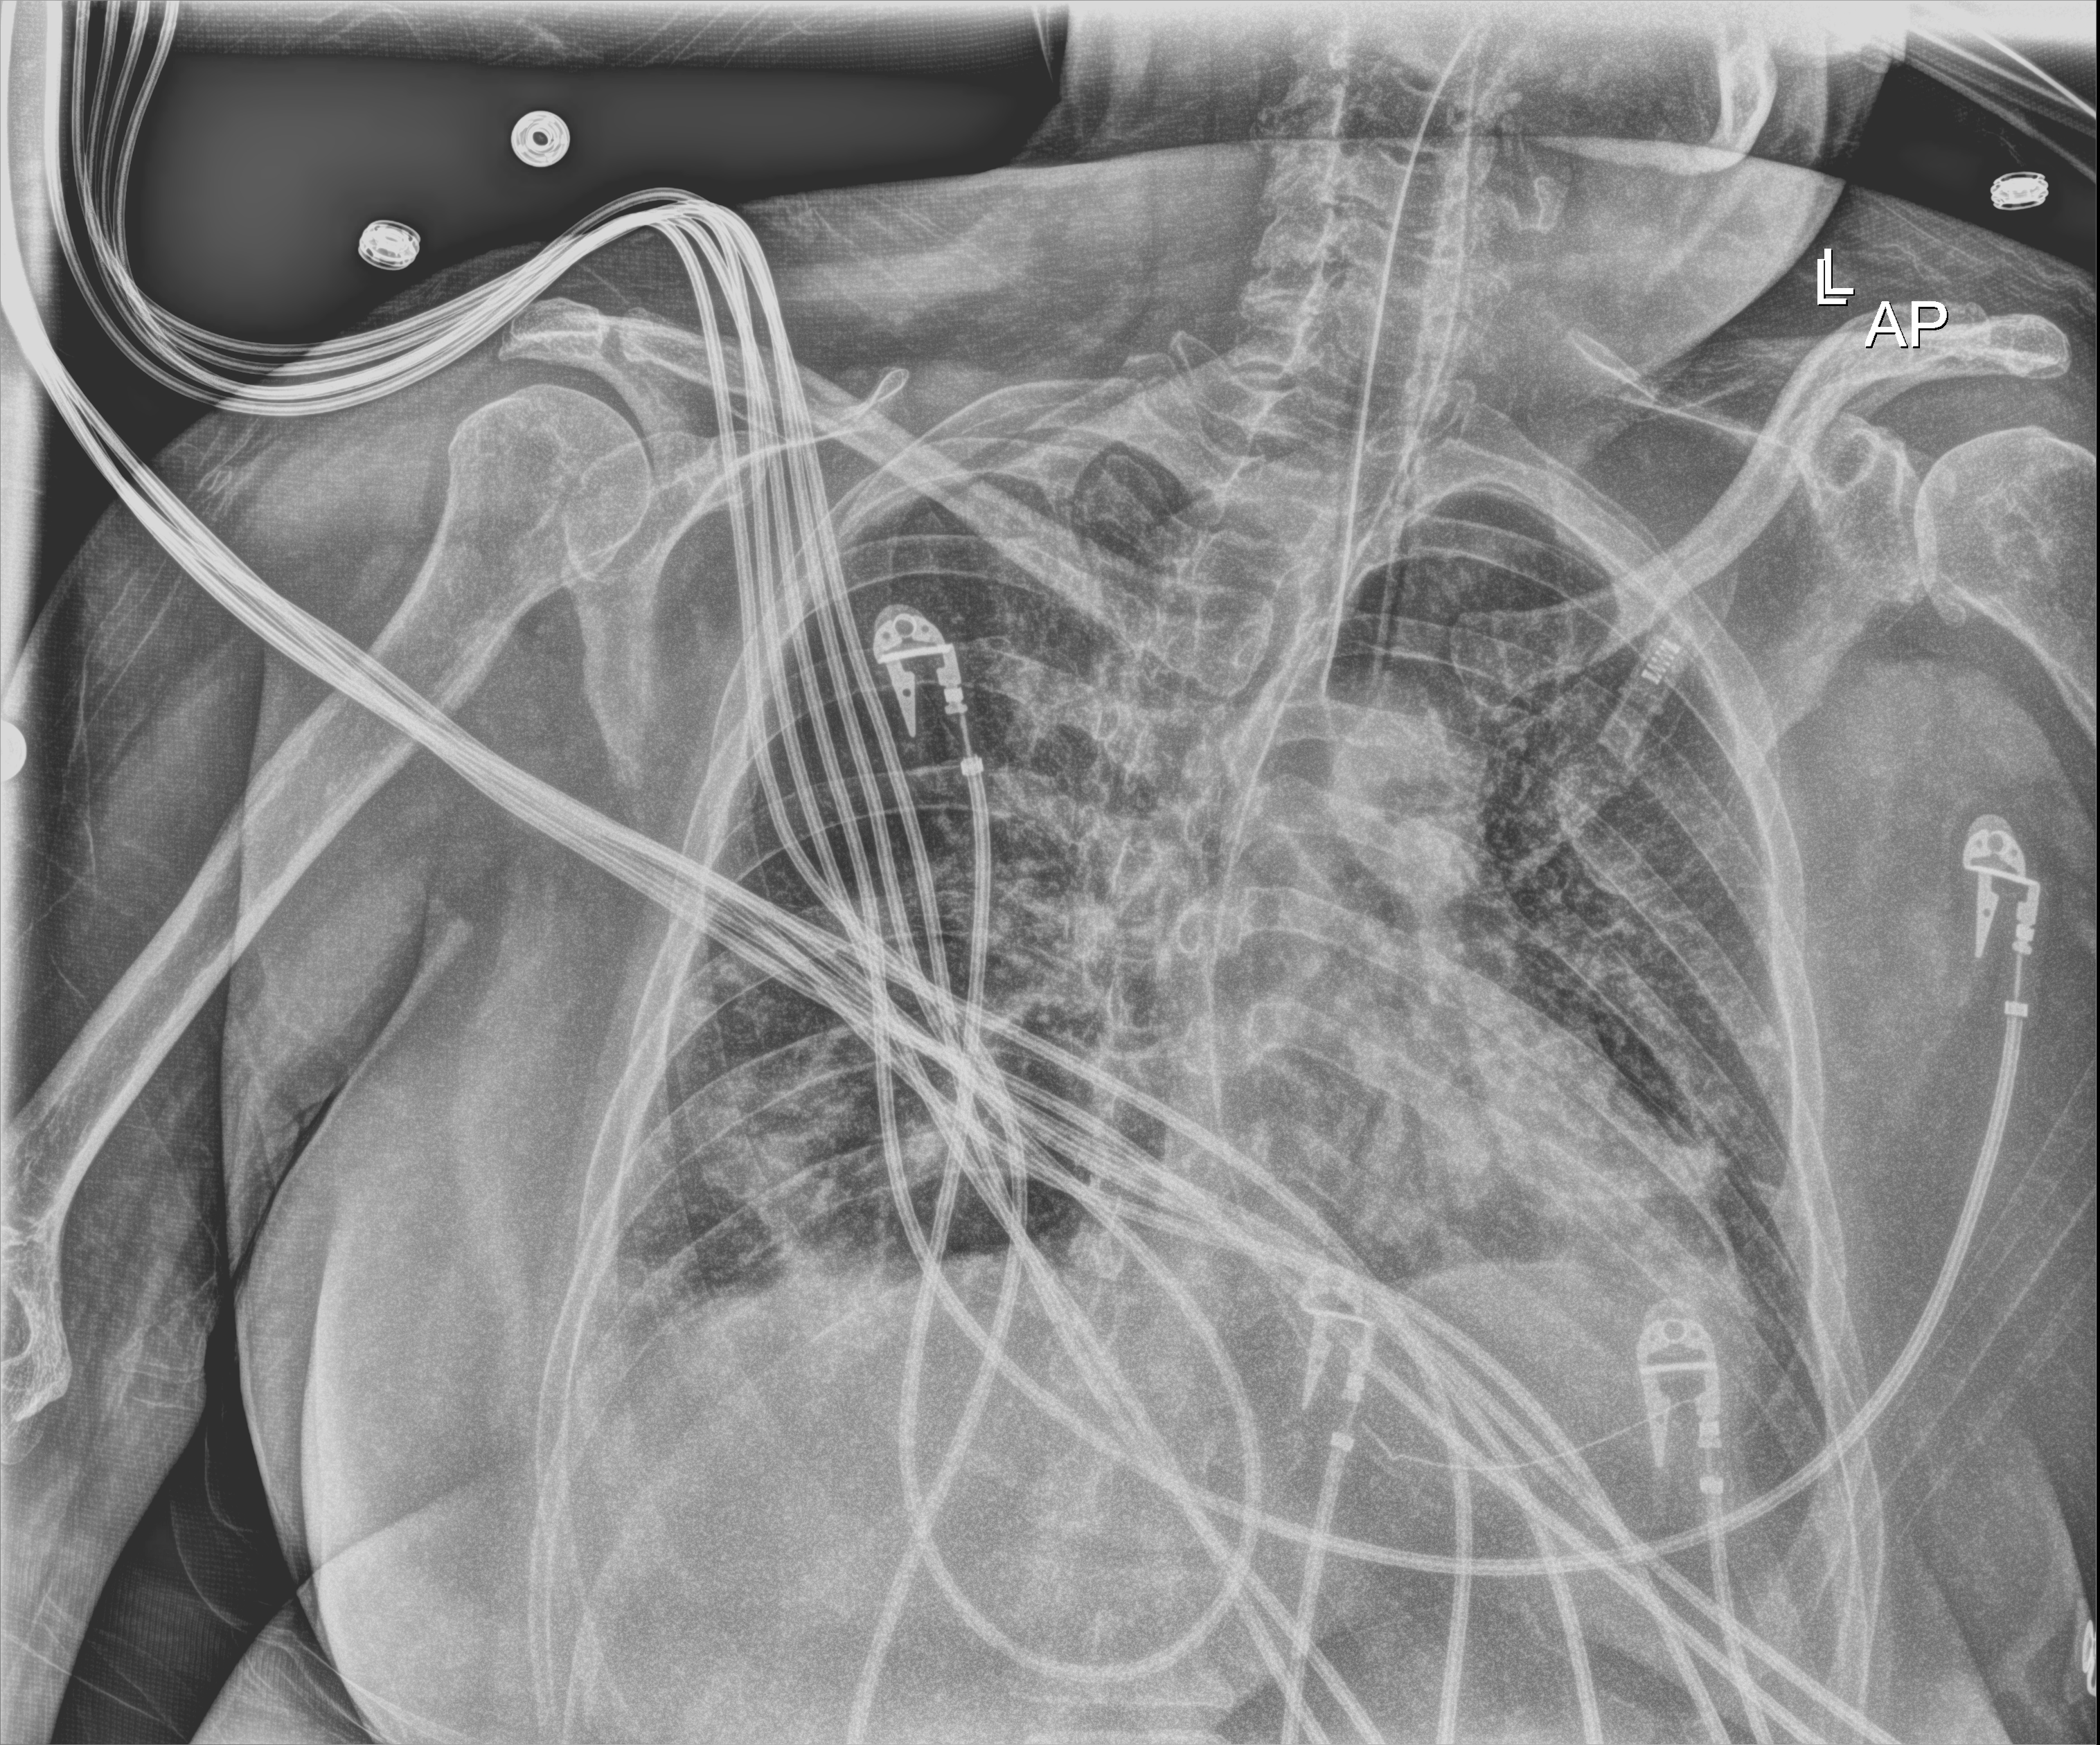
Portable chest radiograph. Adult patient hospitalised with COVID-19, age 18–59 years.
From the hospital-stay record, not from the radiograph (when in the stay this image was taken is not recorded): length of hospital stay: 15 days; mechanically ventilated during this hospital stay: yes; admitted to intensive care during this hospital stay: yes.